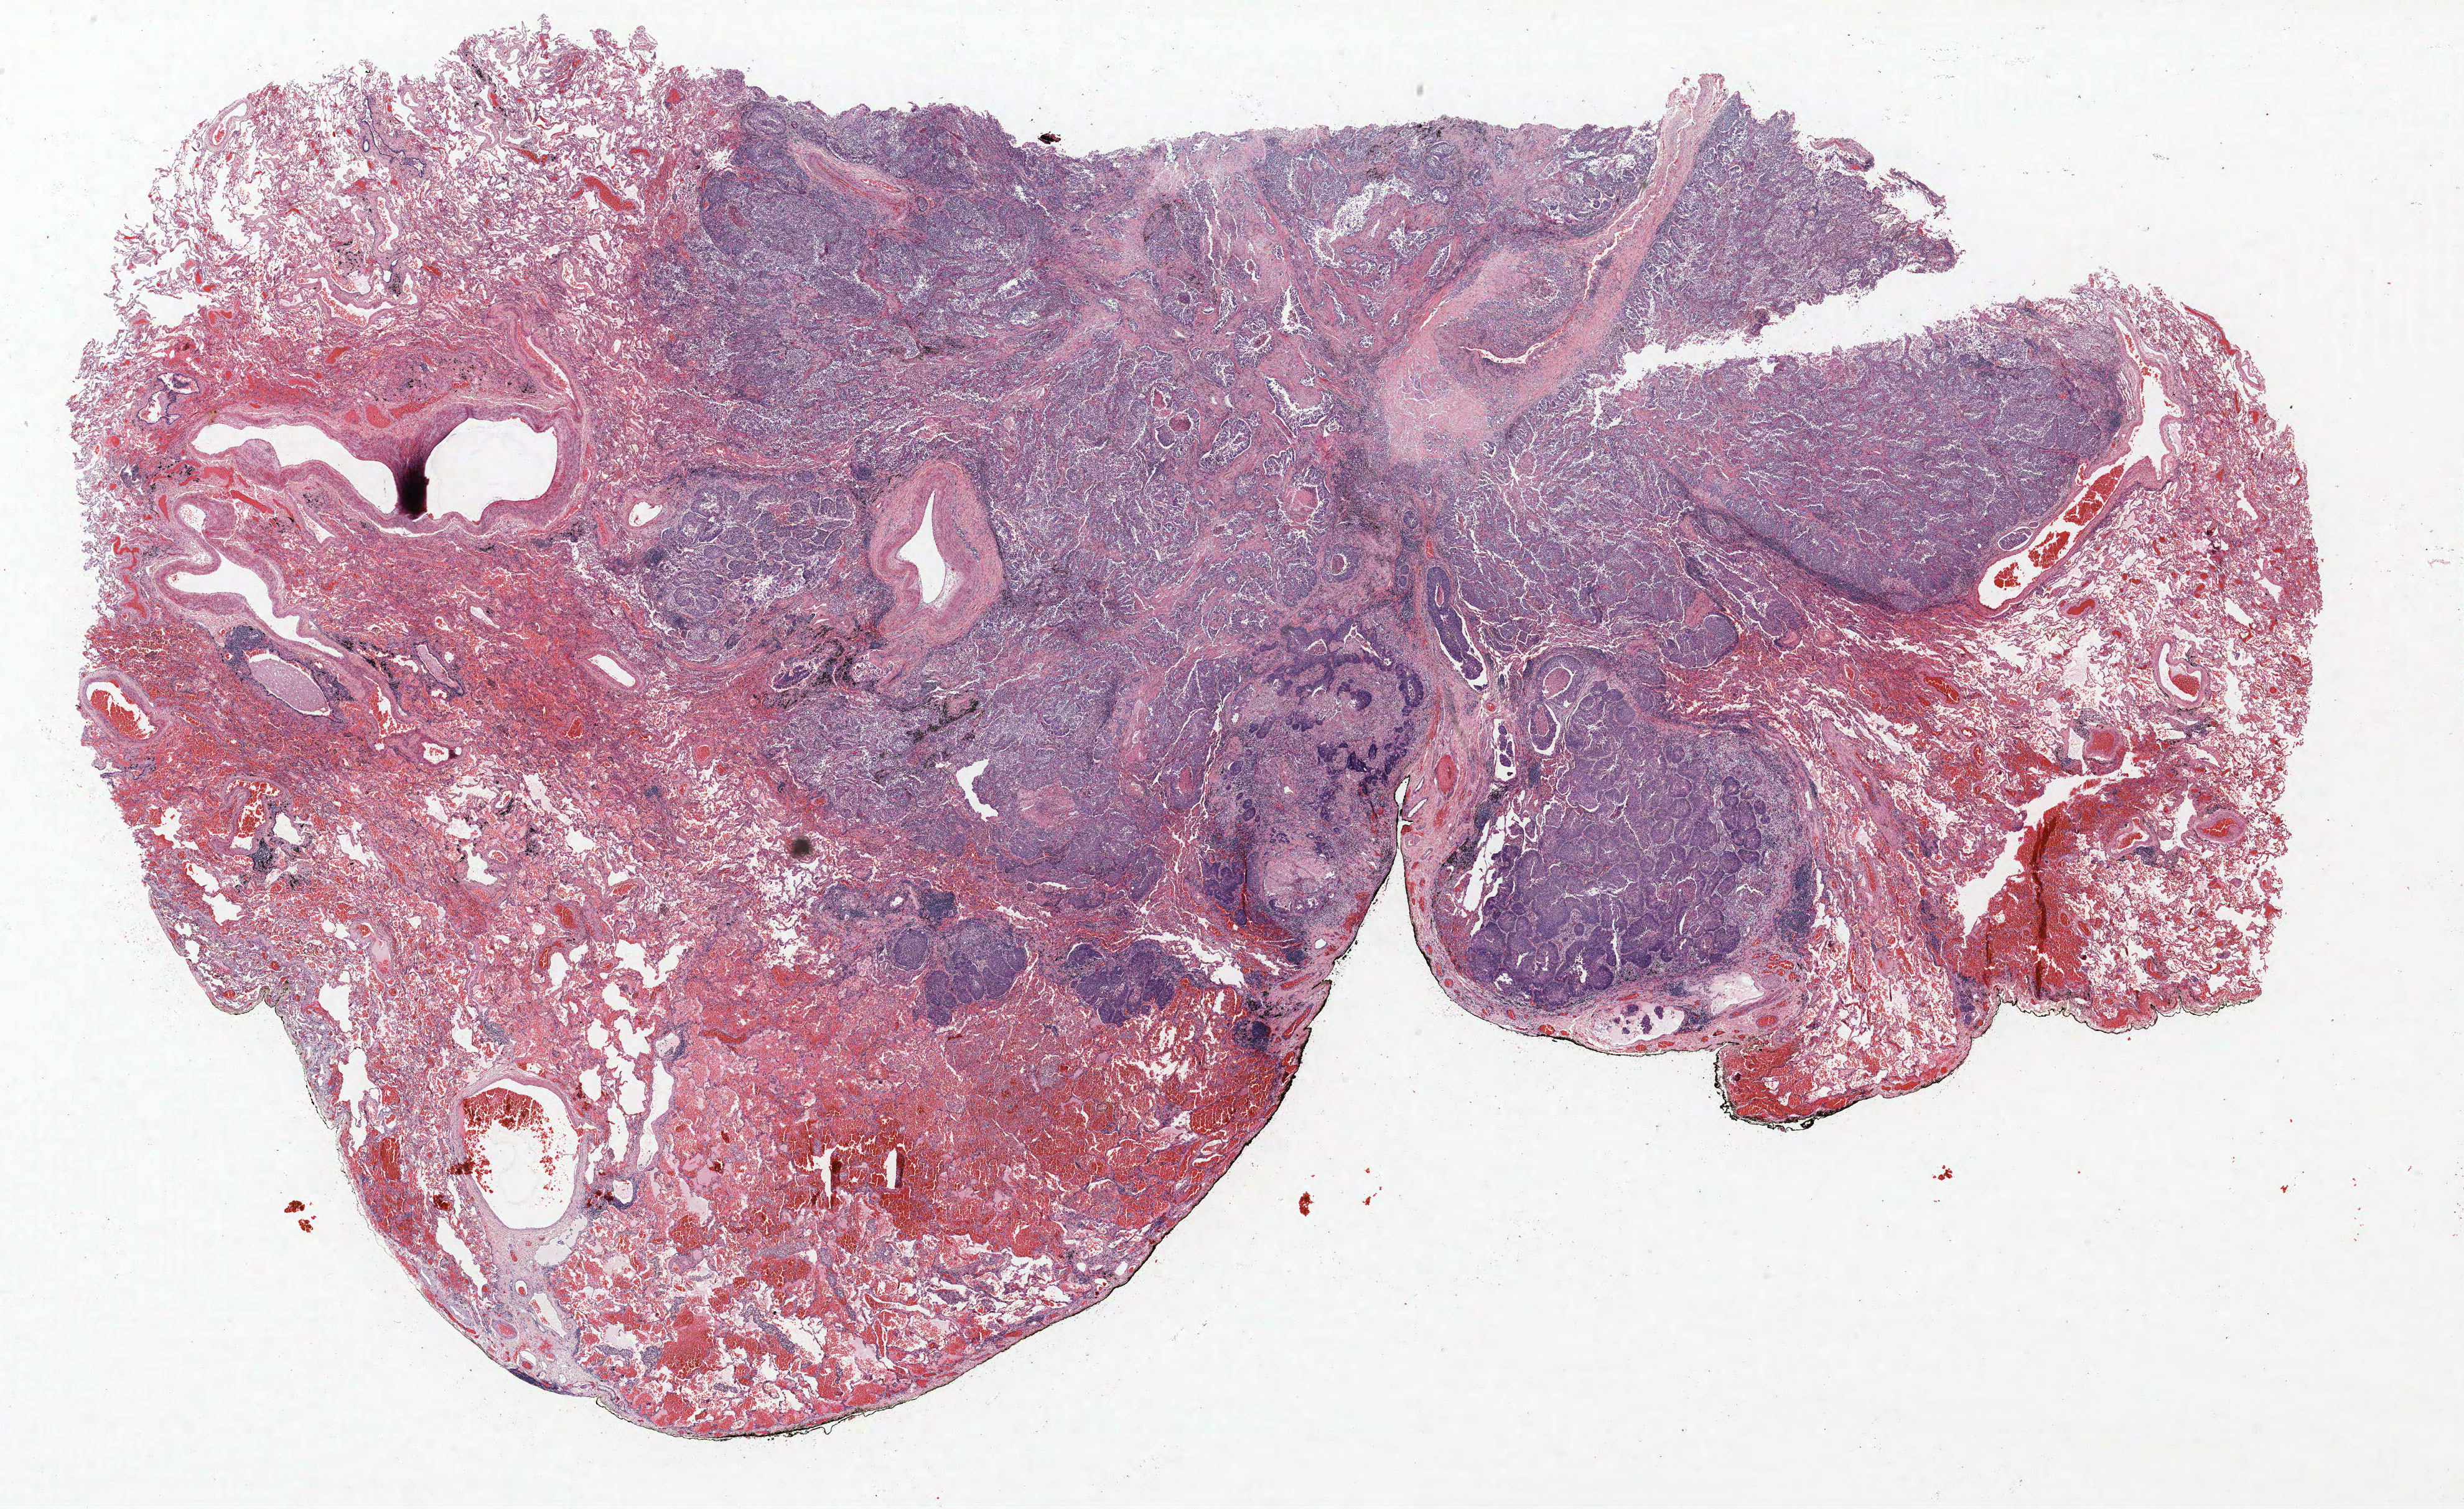
Whole-slide histology image, Hematoxylin and eosin (H&E) stained — whole scanned area (about 31.7 x 19.4 mm, slide scanned at 40x) shown as a low-resolution overview. Formalin-fixed paraffin-embedded (FFPE) section. Lung tissue. Male patient, aged 74 at enrolment. Former smoker at enrolment. Grade: poorly differentiated (G3).
Primary tumour location (clinical record): left upper lobe. Tumour size (pathology): 27 mm. Stage (AJCC 6th edition): IIIA. Participant's lung-cancer diagnosis: Adenocarcinoma, NOS.